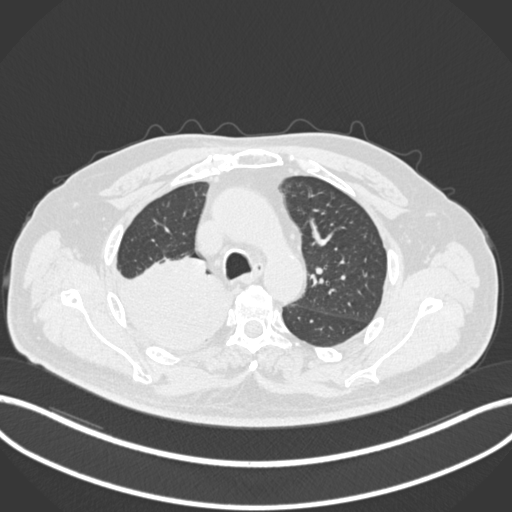
Chest CT, one axial slice. Position 148 of 218 along the scan axis. 120 kVp. Lung window (W 1500 / L -600 HU). 1 mm slice thickness. 512 × 512 image matrix, field of view 400 × 400 mm. Male patient, age 68 years. From the clinical record (not read from this slice): clinical TNM (as recorded): T2a N0 M0.
Annotated regions visible in this slice (rectangle marked by the reading radiologist):
- lung tumour (recorded histology: adenocarcinoma): bounding box <108,255,226,348> (left, top, right, bottom; pixels)